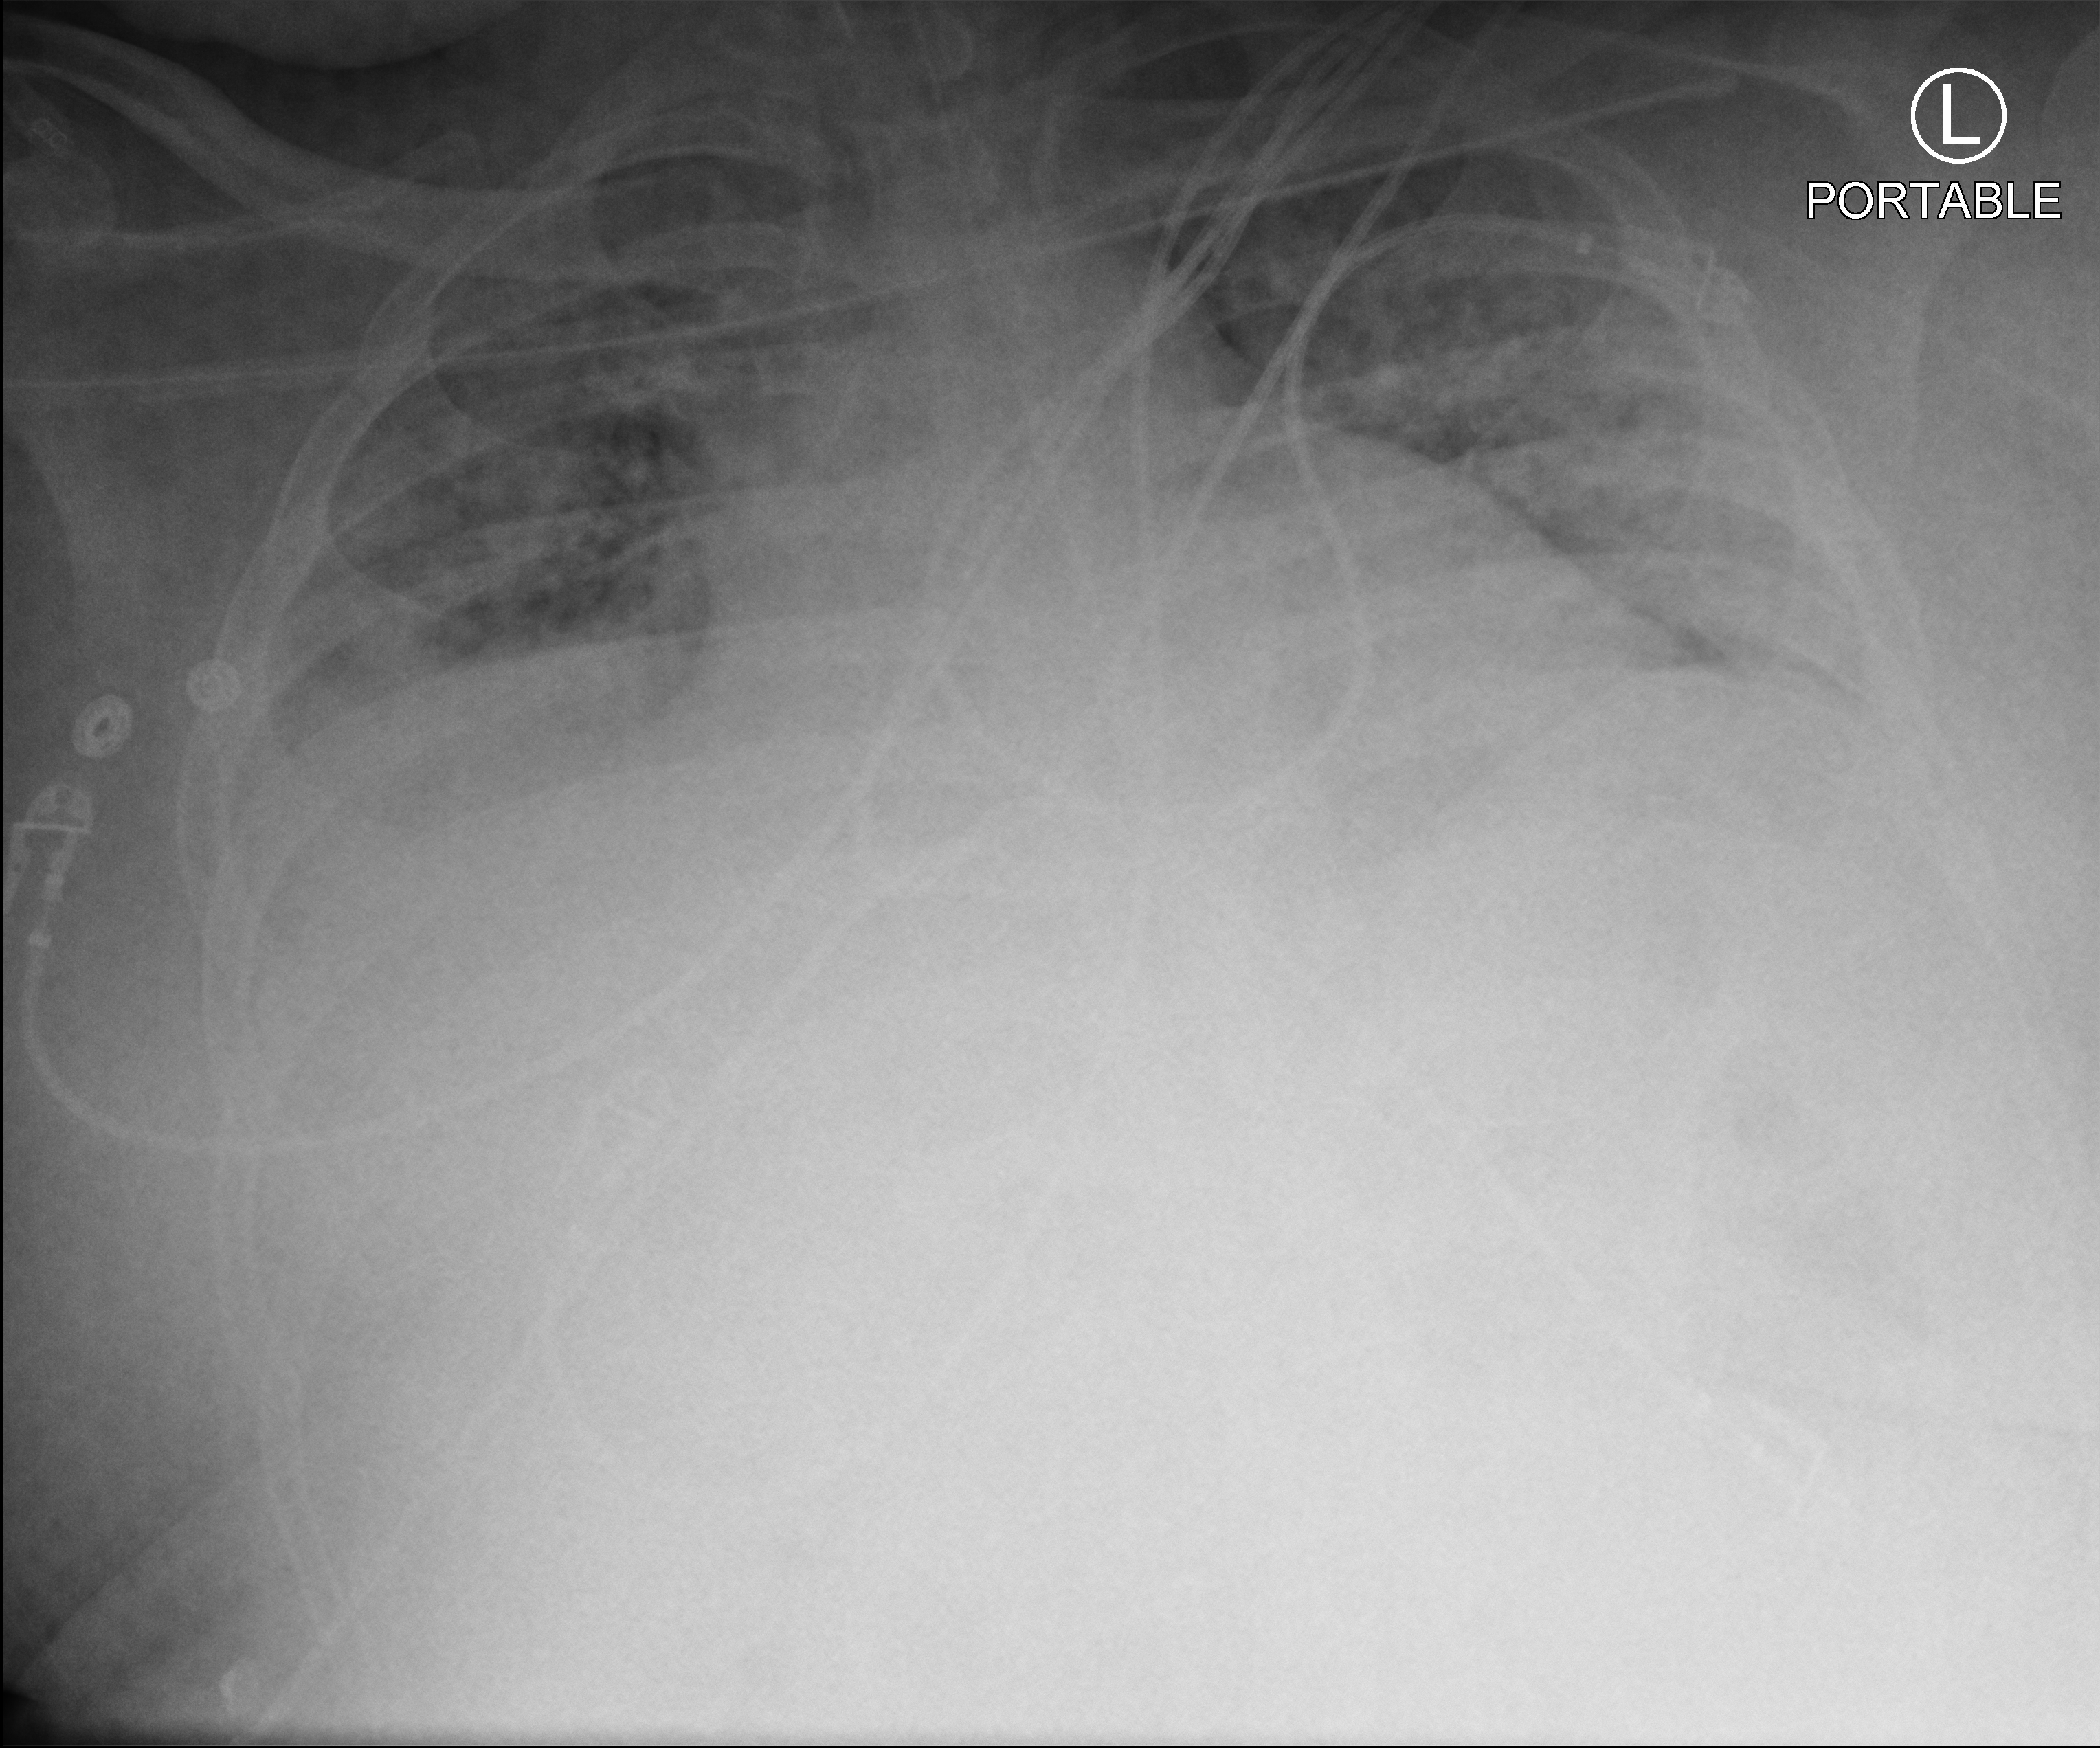
Portable chest radiograph. Male patient hospitalised with COVID-19, age 18–59 years.
Admission-level facts for this patient (not findings on this image; timing relative to this image not recorded): length of hospital stay: 69 days; admitted to intensive care during this hospital stay: yes; diabetes (admission record): yes.